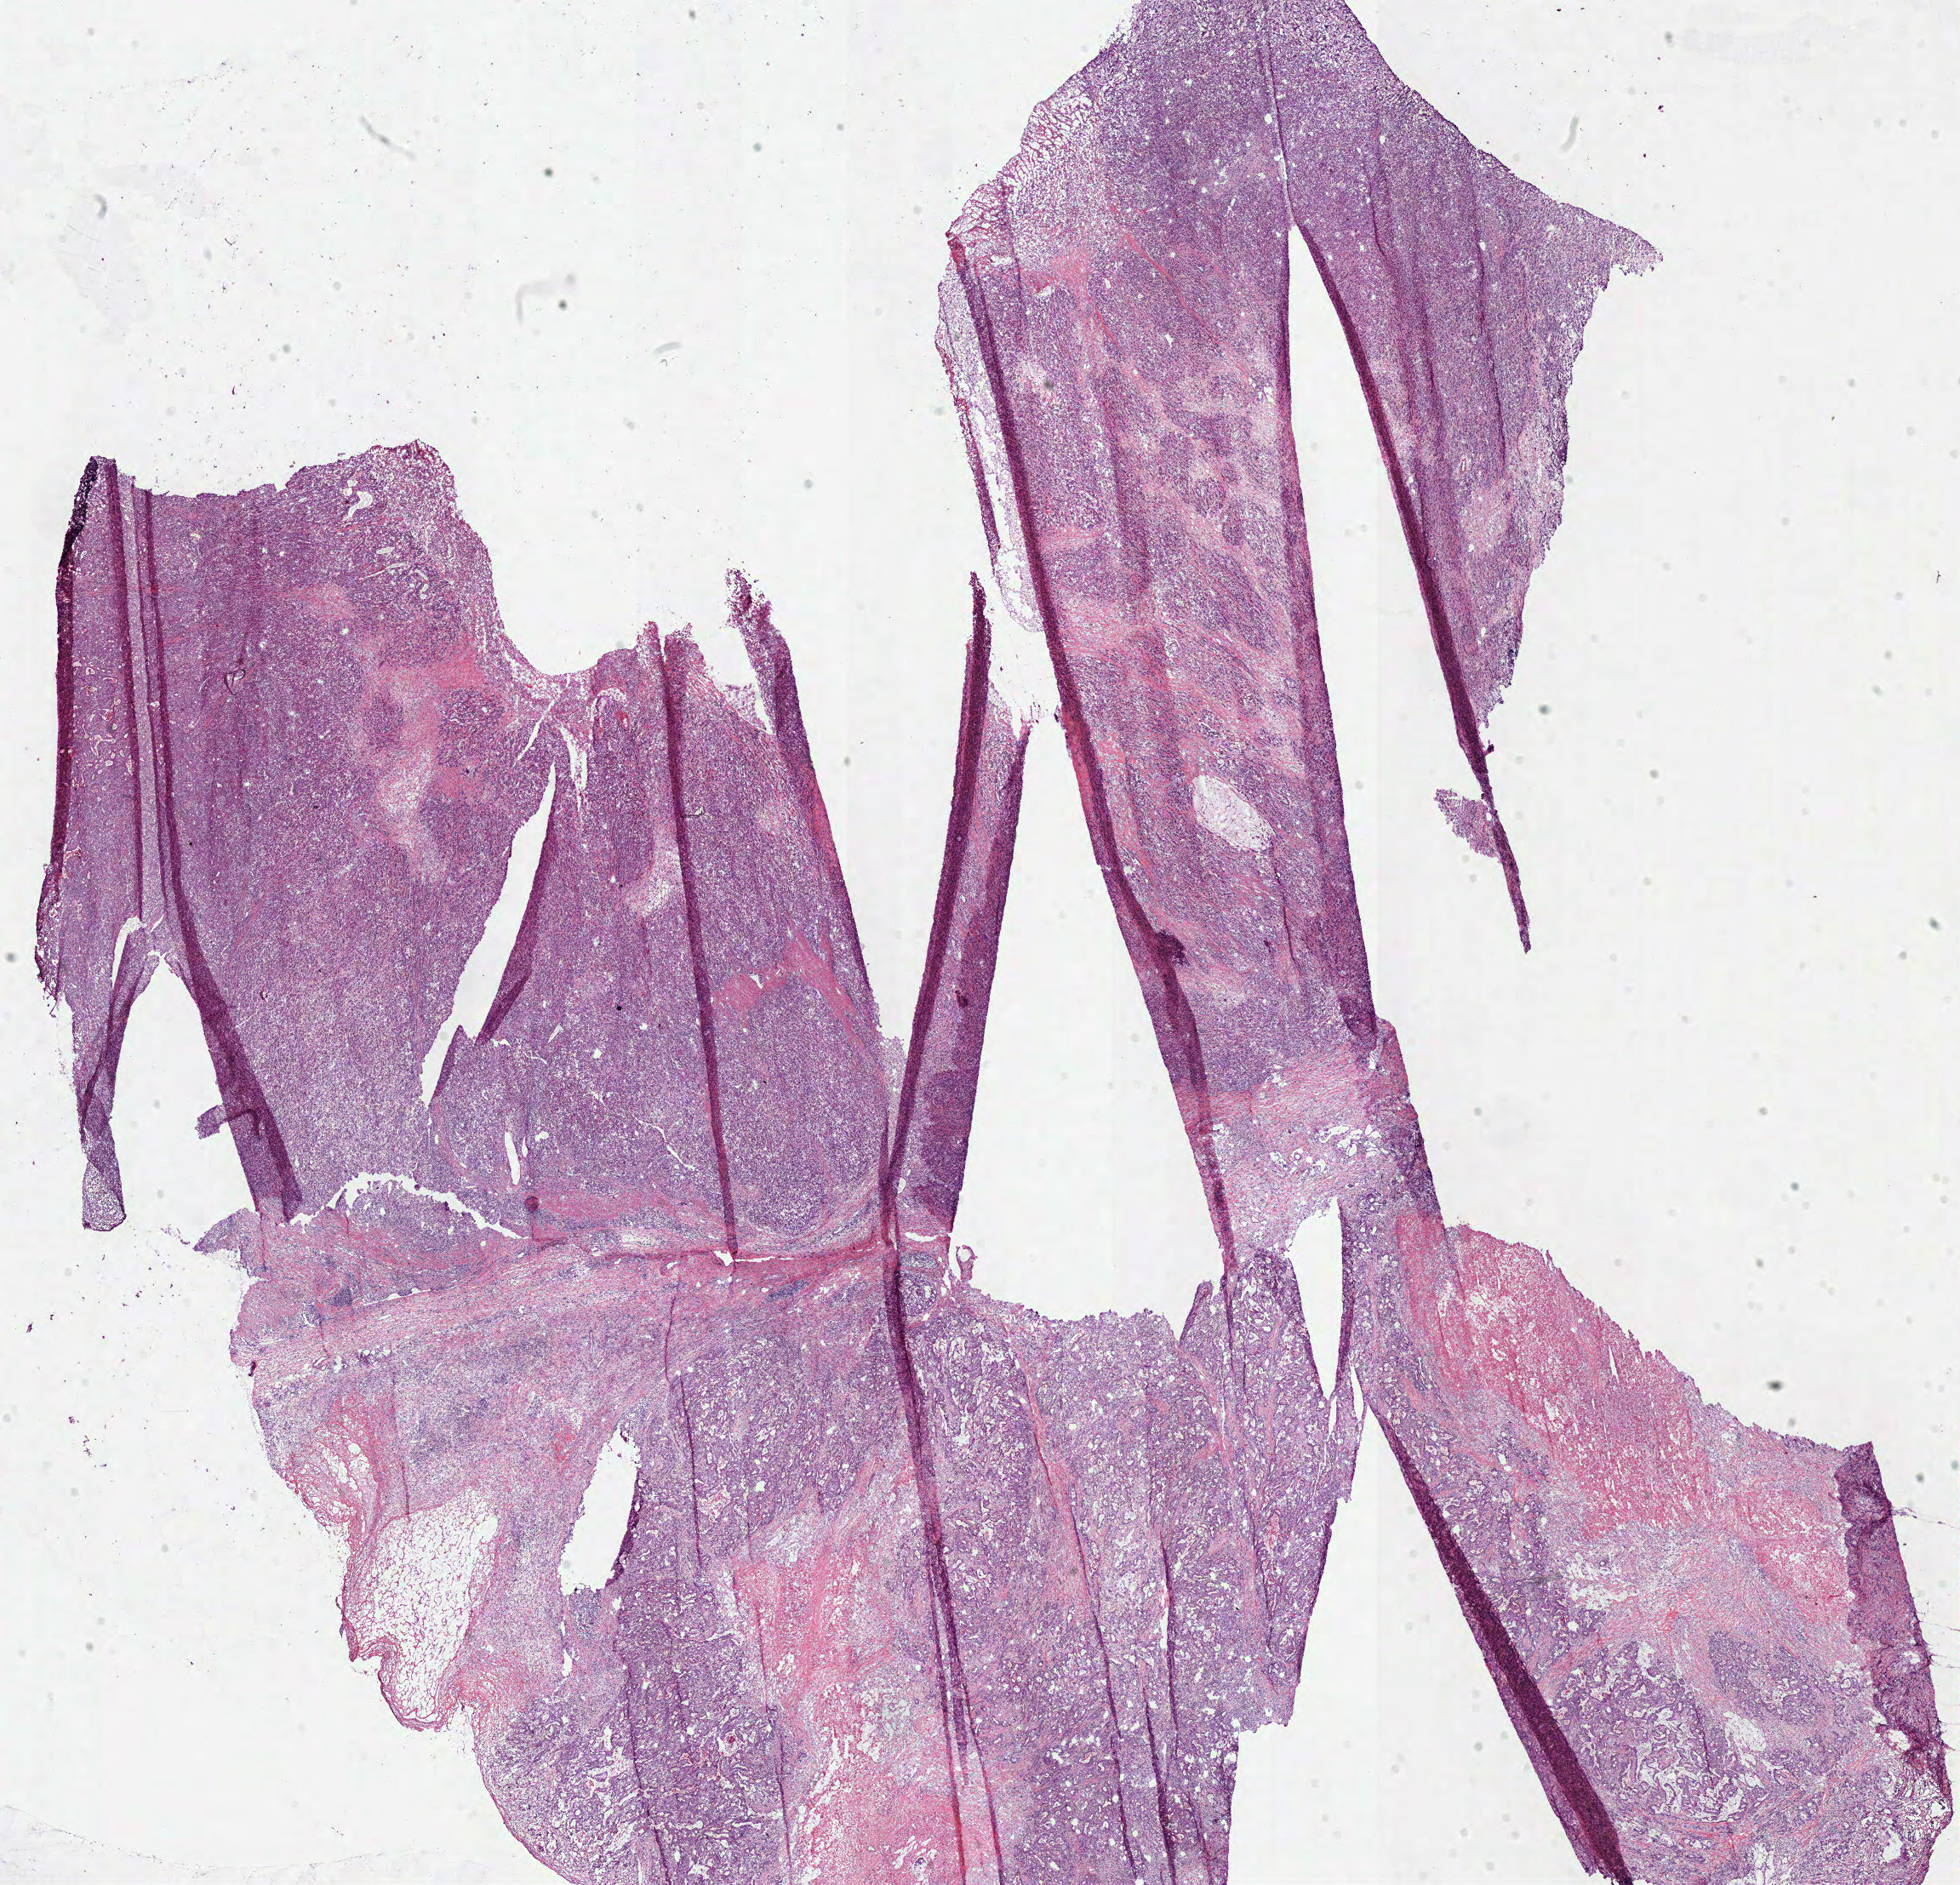
H&E-stained whole-slide image, shown as a low-resolution overview of the whole scanned area (about 18.1 x 17.4 mm, slide scanned at 40x), frozen section, sample: primary tumour, colon. Female, age 78 years at initial diagnosis. Composition of this section per pathologist review: tumour cells 70%, tumour nuclei 80%, normal cells 0%, stromal cells 15%, necrosis 15%.
Lymph nodes positive (case pathology): 0 of 16 examined. AJCC pathologic stage: IIA. Histologic diagnosis: Adenocarcinoma, NOS.